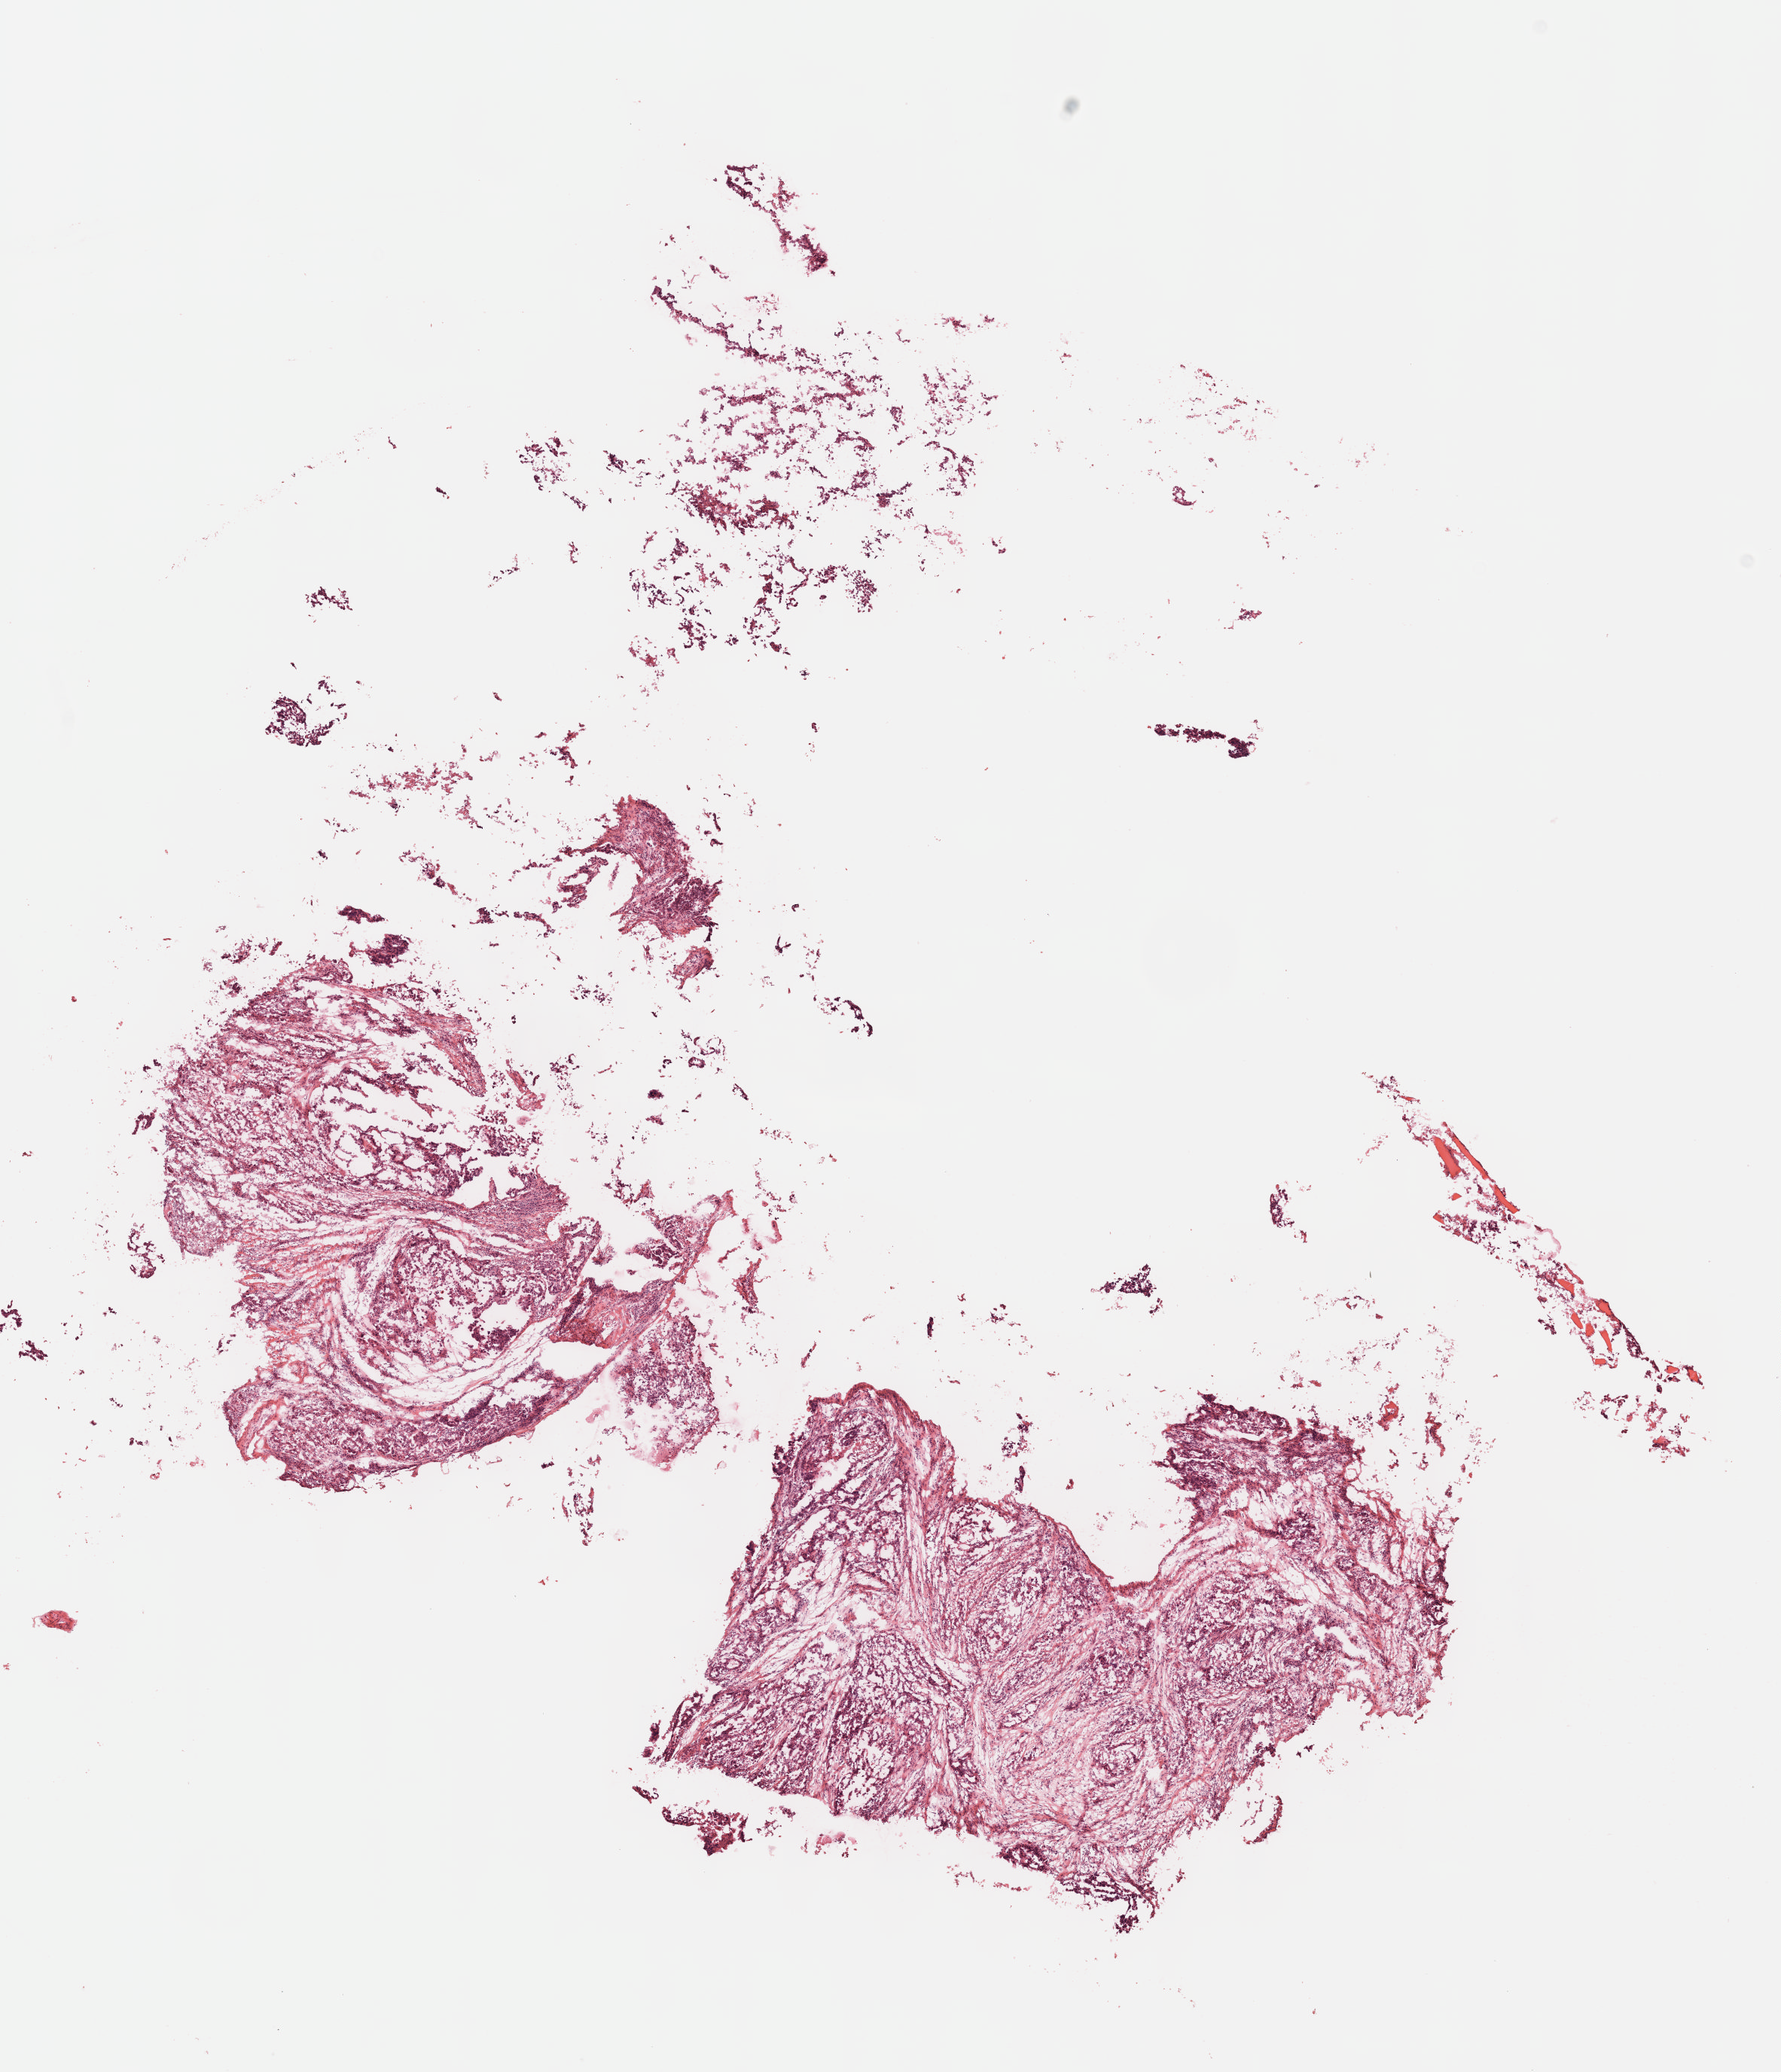
H&E whole-slide image — a low-resolution overview of the entire scanned area, about 9.6 x 11.1 mm (from a 40x scan); formalin-fixed paraffin-embedded (FFPE) diagnostic section; primary tumour sample from the stomach. Female patient; age at initial diagnosis 82 years. Histologic grade: G3 (poorly differentiated).
TNM: T3 N1 M0. Diagnosis: Mucinous adenocarcinoma (gastric antrum). Lymph nodes positive (case pathology): 2 of 2 examined. AJCC pathologic stage: IIIA.